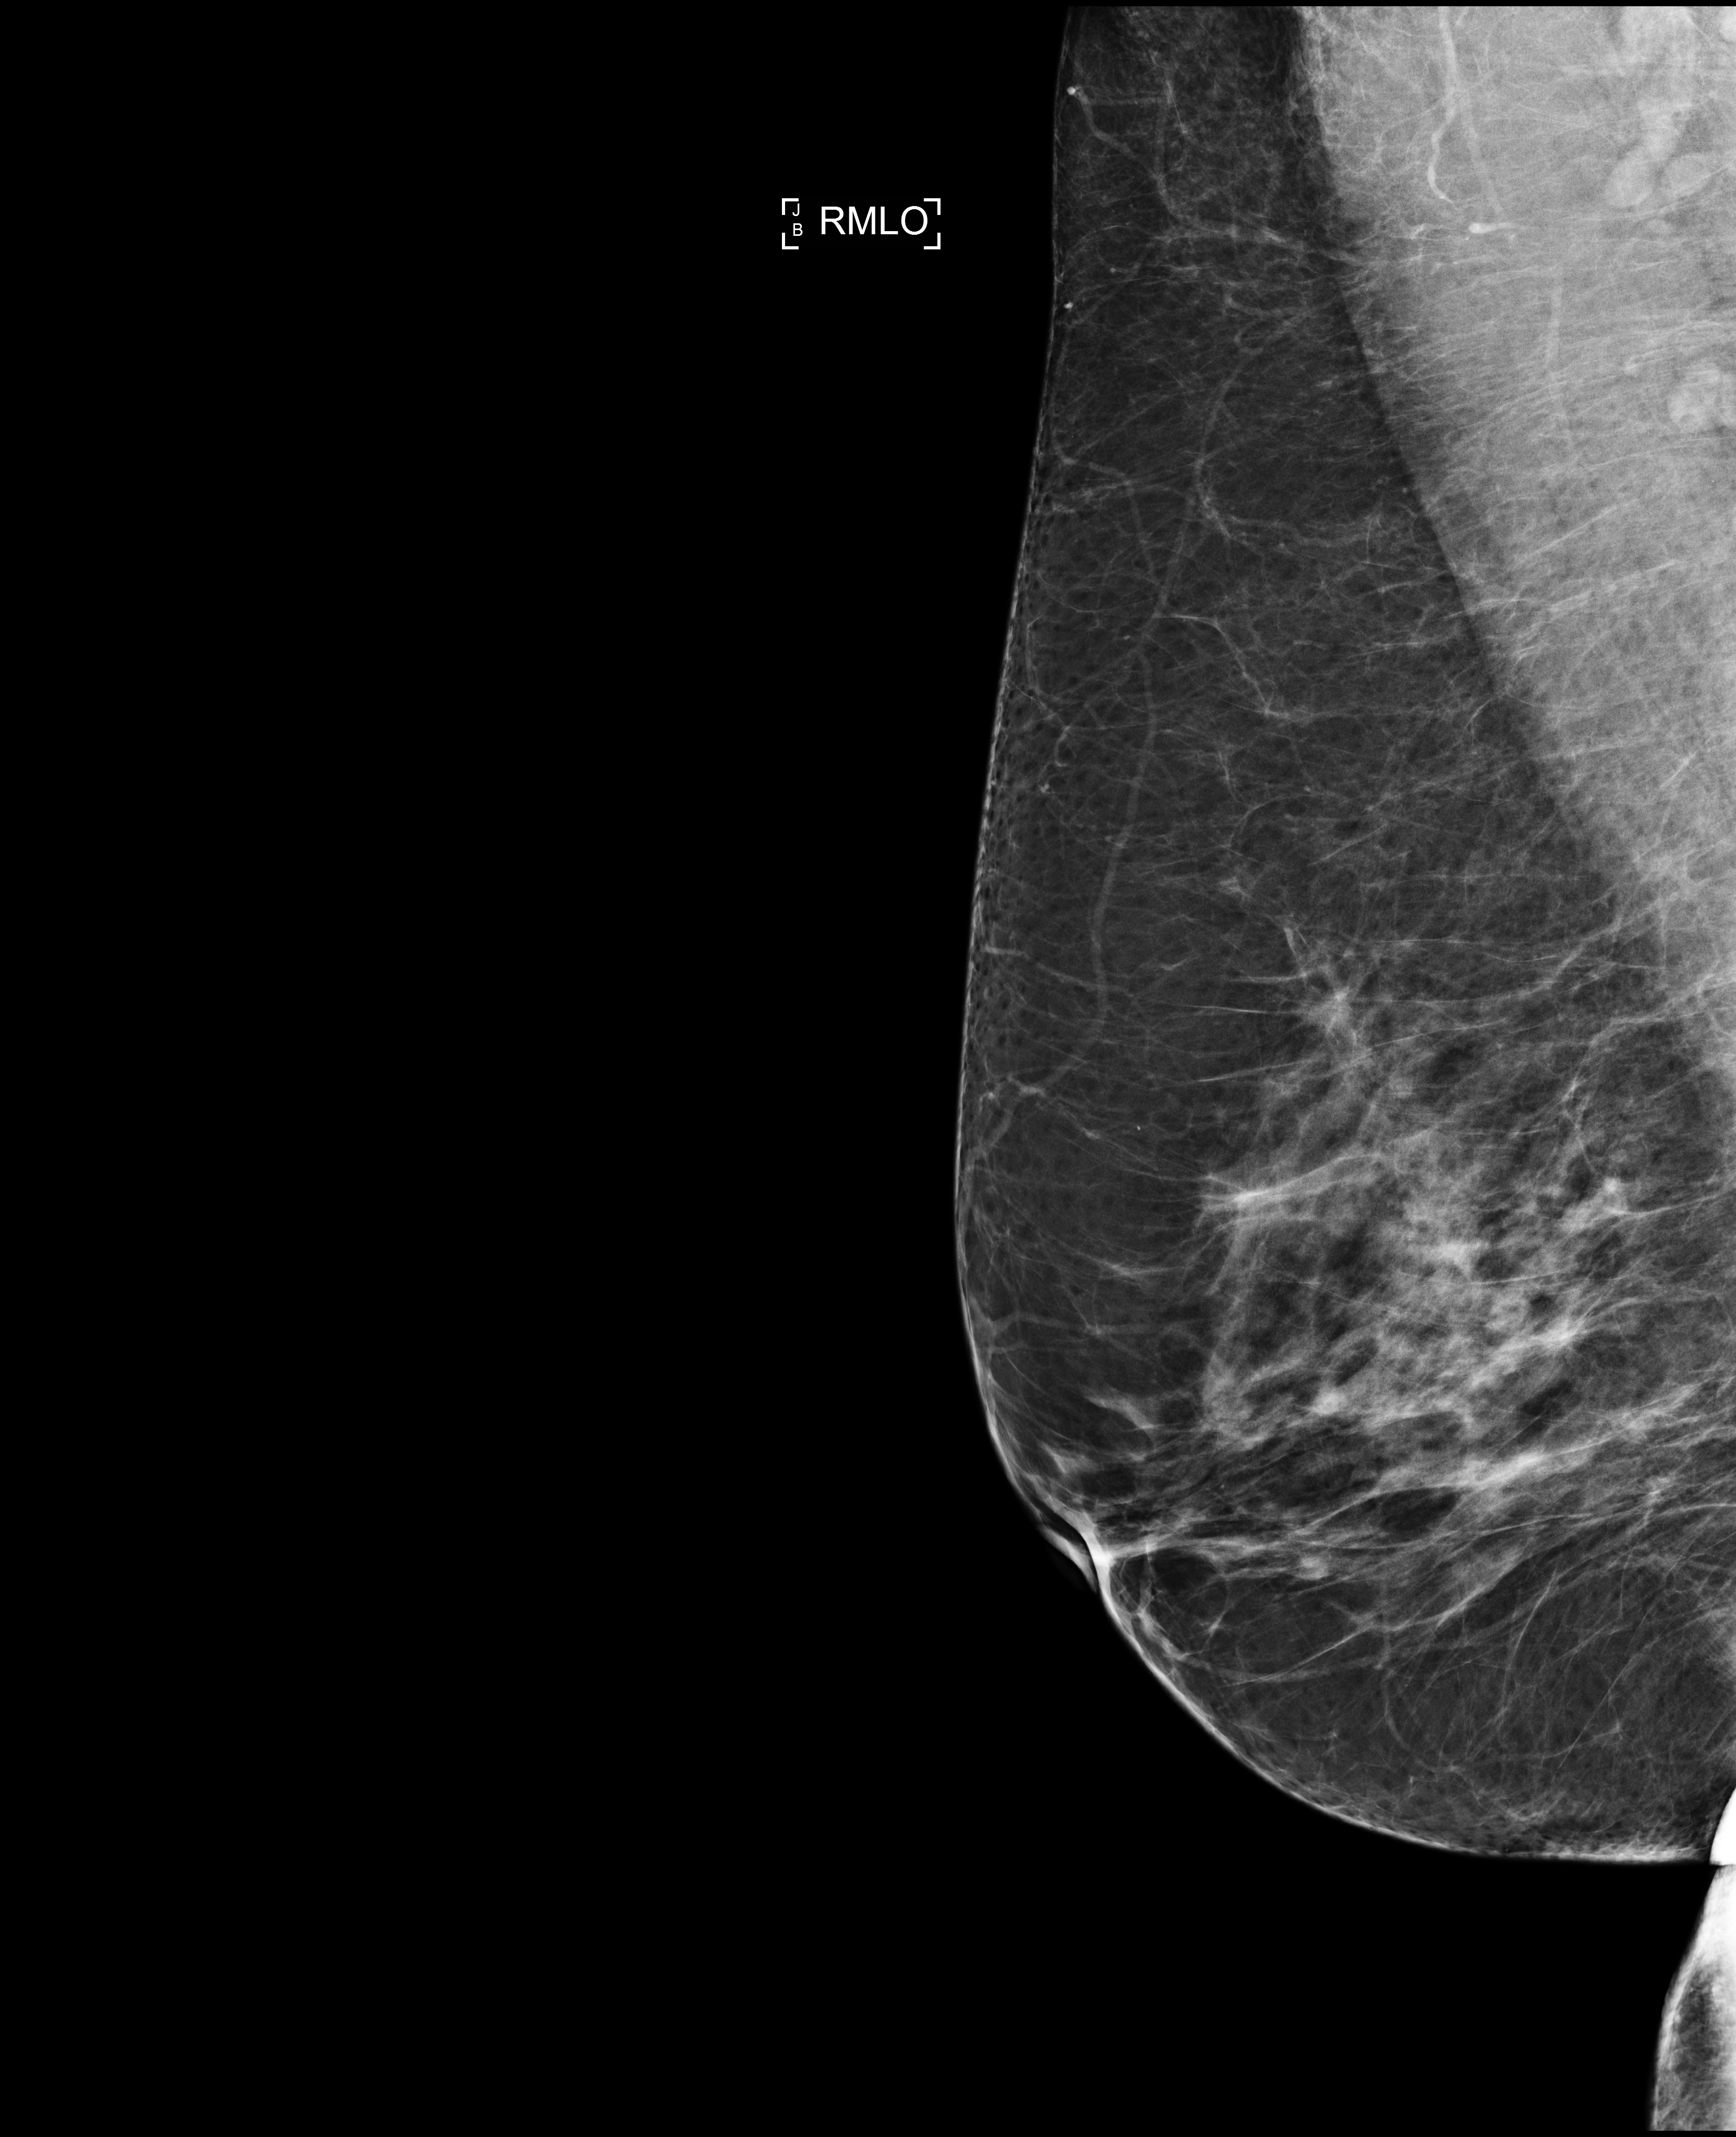
Full-field digital mammogram (FFDM); right breast; mediolateral oblique (MLO) view; screening examination; compressed breast thickness 74 mm. Female patient, age 55 years.
Breast density at the screening exam (both breasts): heterogeneously dense (BI-RADS density category c). Final BI-RADS assessment for this screening round (tomosynthesis exam, both breasts): category 1. Recall: no recall after this screen.